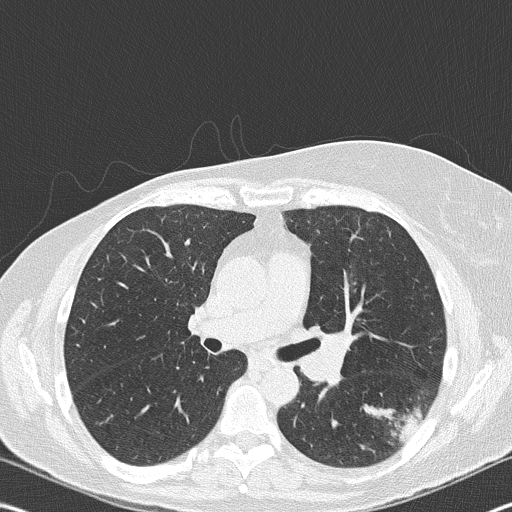
Low-dose screening chest CT, one axial slice. Slice 106 of 177 in the series (ordered by position). Reconstruction kernel B50f. 120 kVp. Lung window (W 1500 / L -600 HU). 2 mm slice thickness. 512 × 512 image matrix.
Outlined on this slice (expert manual segmentation):
- lesion 1 (tumor): bounding box [x1, y1, x2, y2] px = [363, 405, 422, 444]
- lesion 2 (nodule, hilum of left lung): [305, 335, 346, 380]